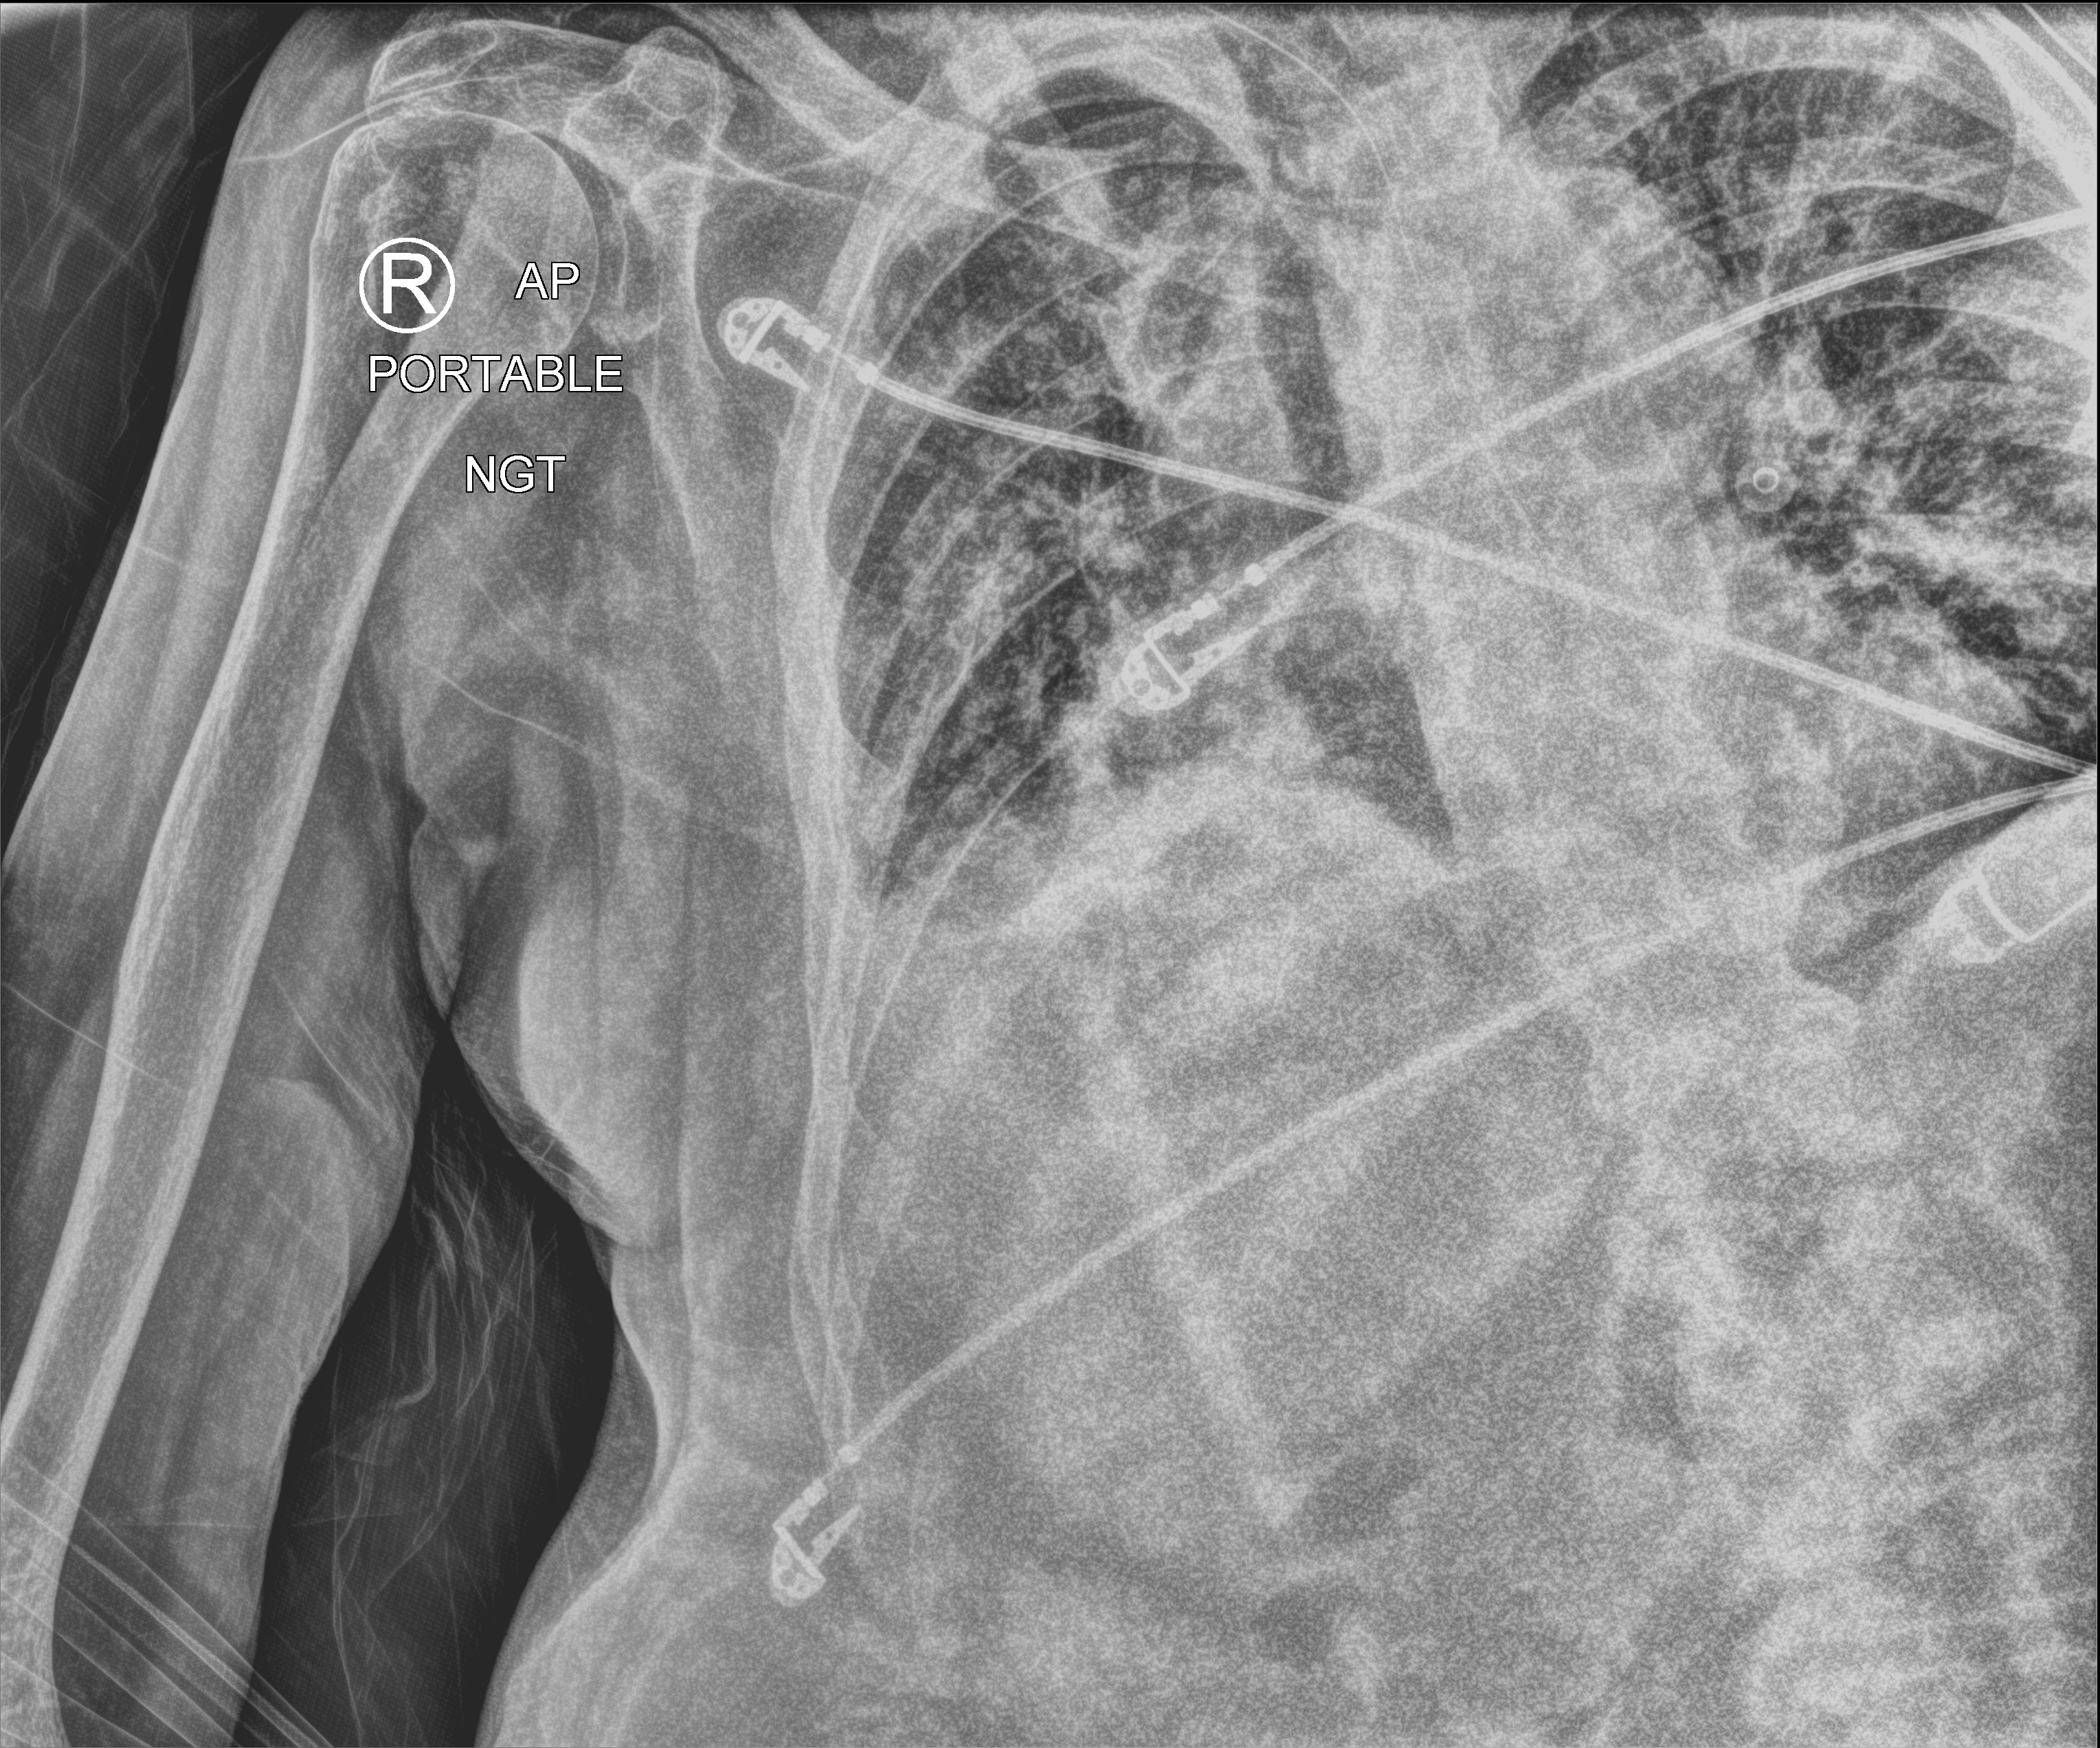
Portable chest radiograph; anteroposterior (AP) projection. Male patient hospitalised with COVID-19, age 75–90 years.
Admission-level facts for this patient (not findings on this image; timing relative to this image not recorded): mechanically ventilated during this hospital stay: no; admitted to intensive care during this hospital stay: no.